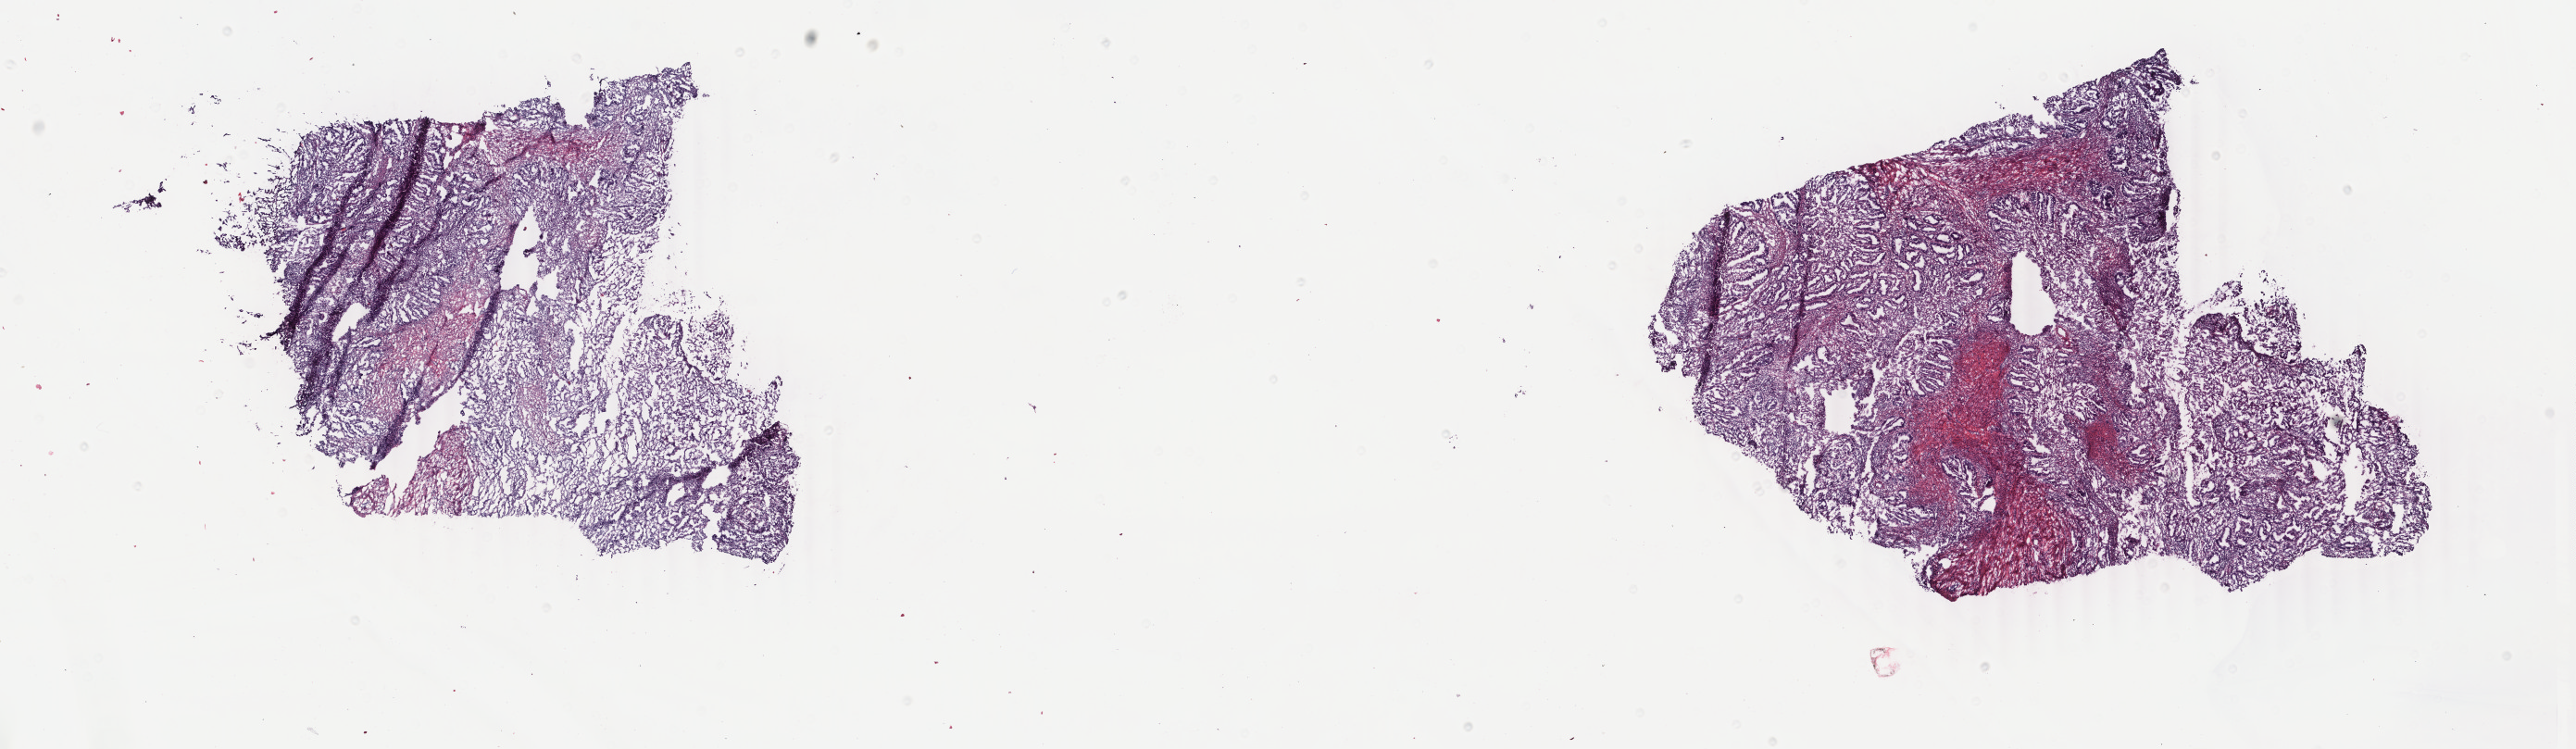
Hematoxylin and eosin (H&E) stained whole-slide image, a low-resolution overview of the entire scanned area, about 22.1 x 6.4 mm (slide scanned at 40x); frozen section from the bottom of the tissue portion; sample: primary tumour, uterus. Female, age 81 years at initial diagnosis. Histologic grade: G2 (moderately differentiated). Slide review estimates, as recorded: tumour cells 70%, tumour nuclei 70%, normal cells 0%, stromal cells 20%, necrosis 10%. Inflammatory infiltration, as recorded: lymphocyte infiltration 30%, monocyte infiltration 30%, neutrophil infiltration 30%.
Pathologic diagnosis: Endometrioid adenocarcinoma, NOS (endometrium). FIGO stage: IB.